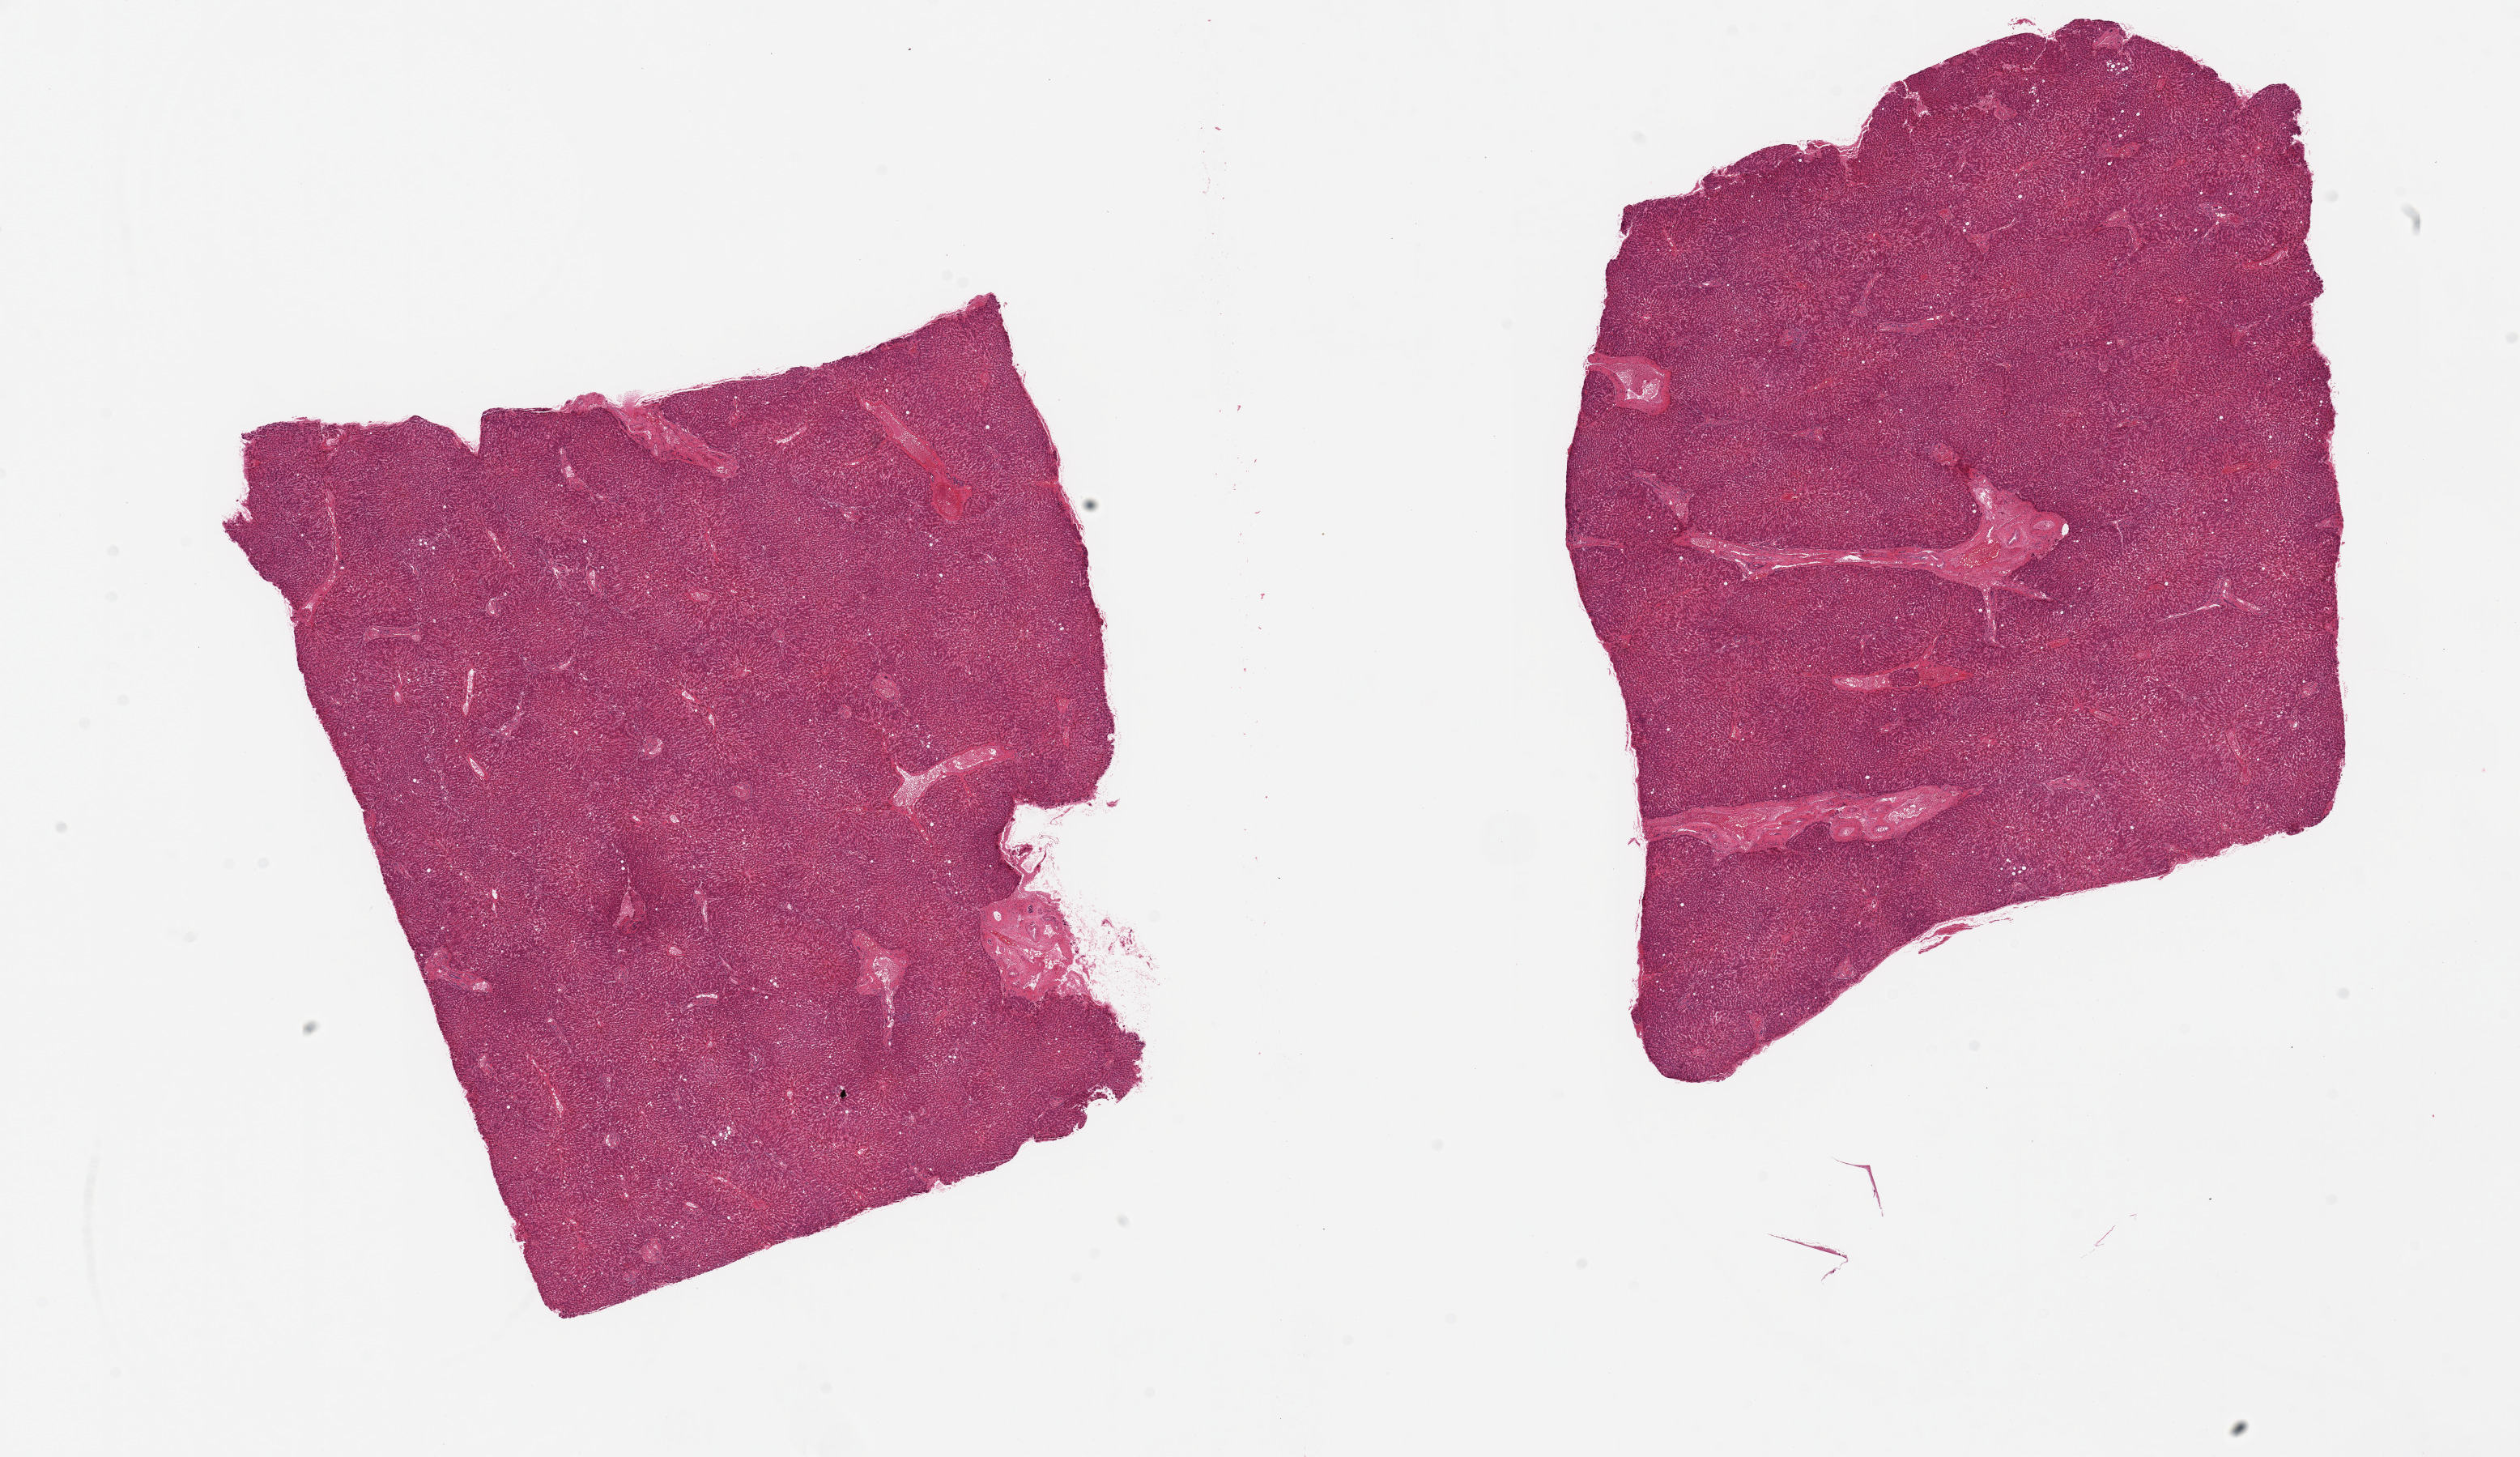
Digitized hematoxylin and eosin (H&E)-stained section, a low-resolution overview of the entire scanned area, about 24.6 x 14.2 mm. PAXgene-fixed, paraffin-embedded tissue. Target tissue: liver. Donor tissue sample. Male donor.
- reviewer comment on this tissue sample: 2 pieces. 9x8 & 10x8mm; minimal steatosis